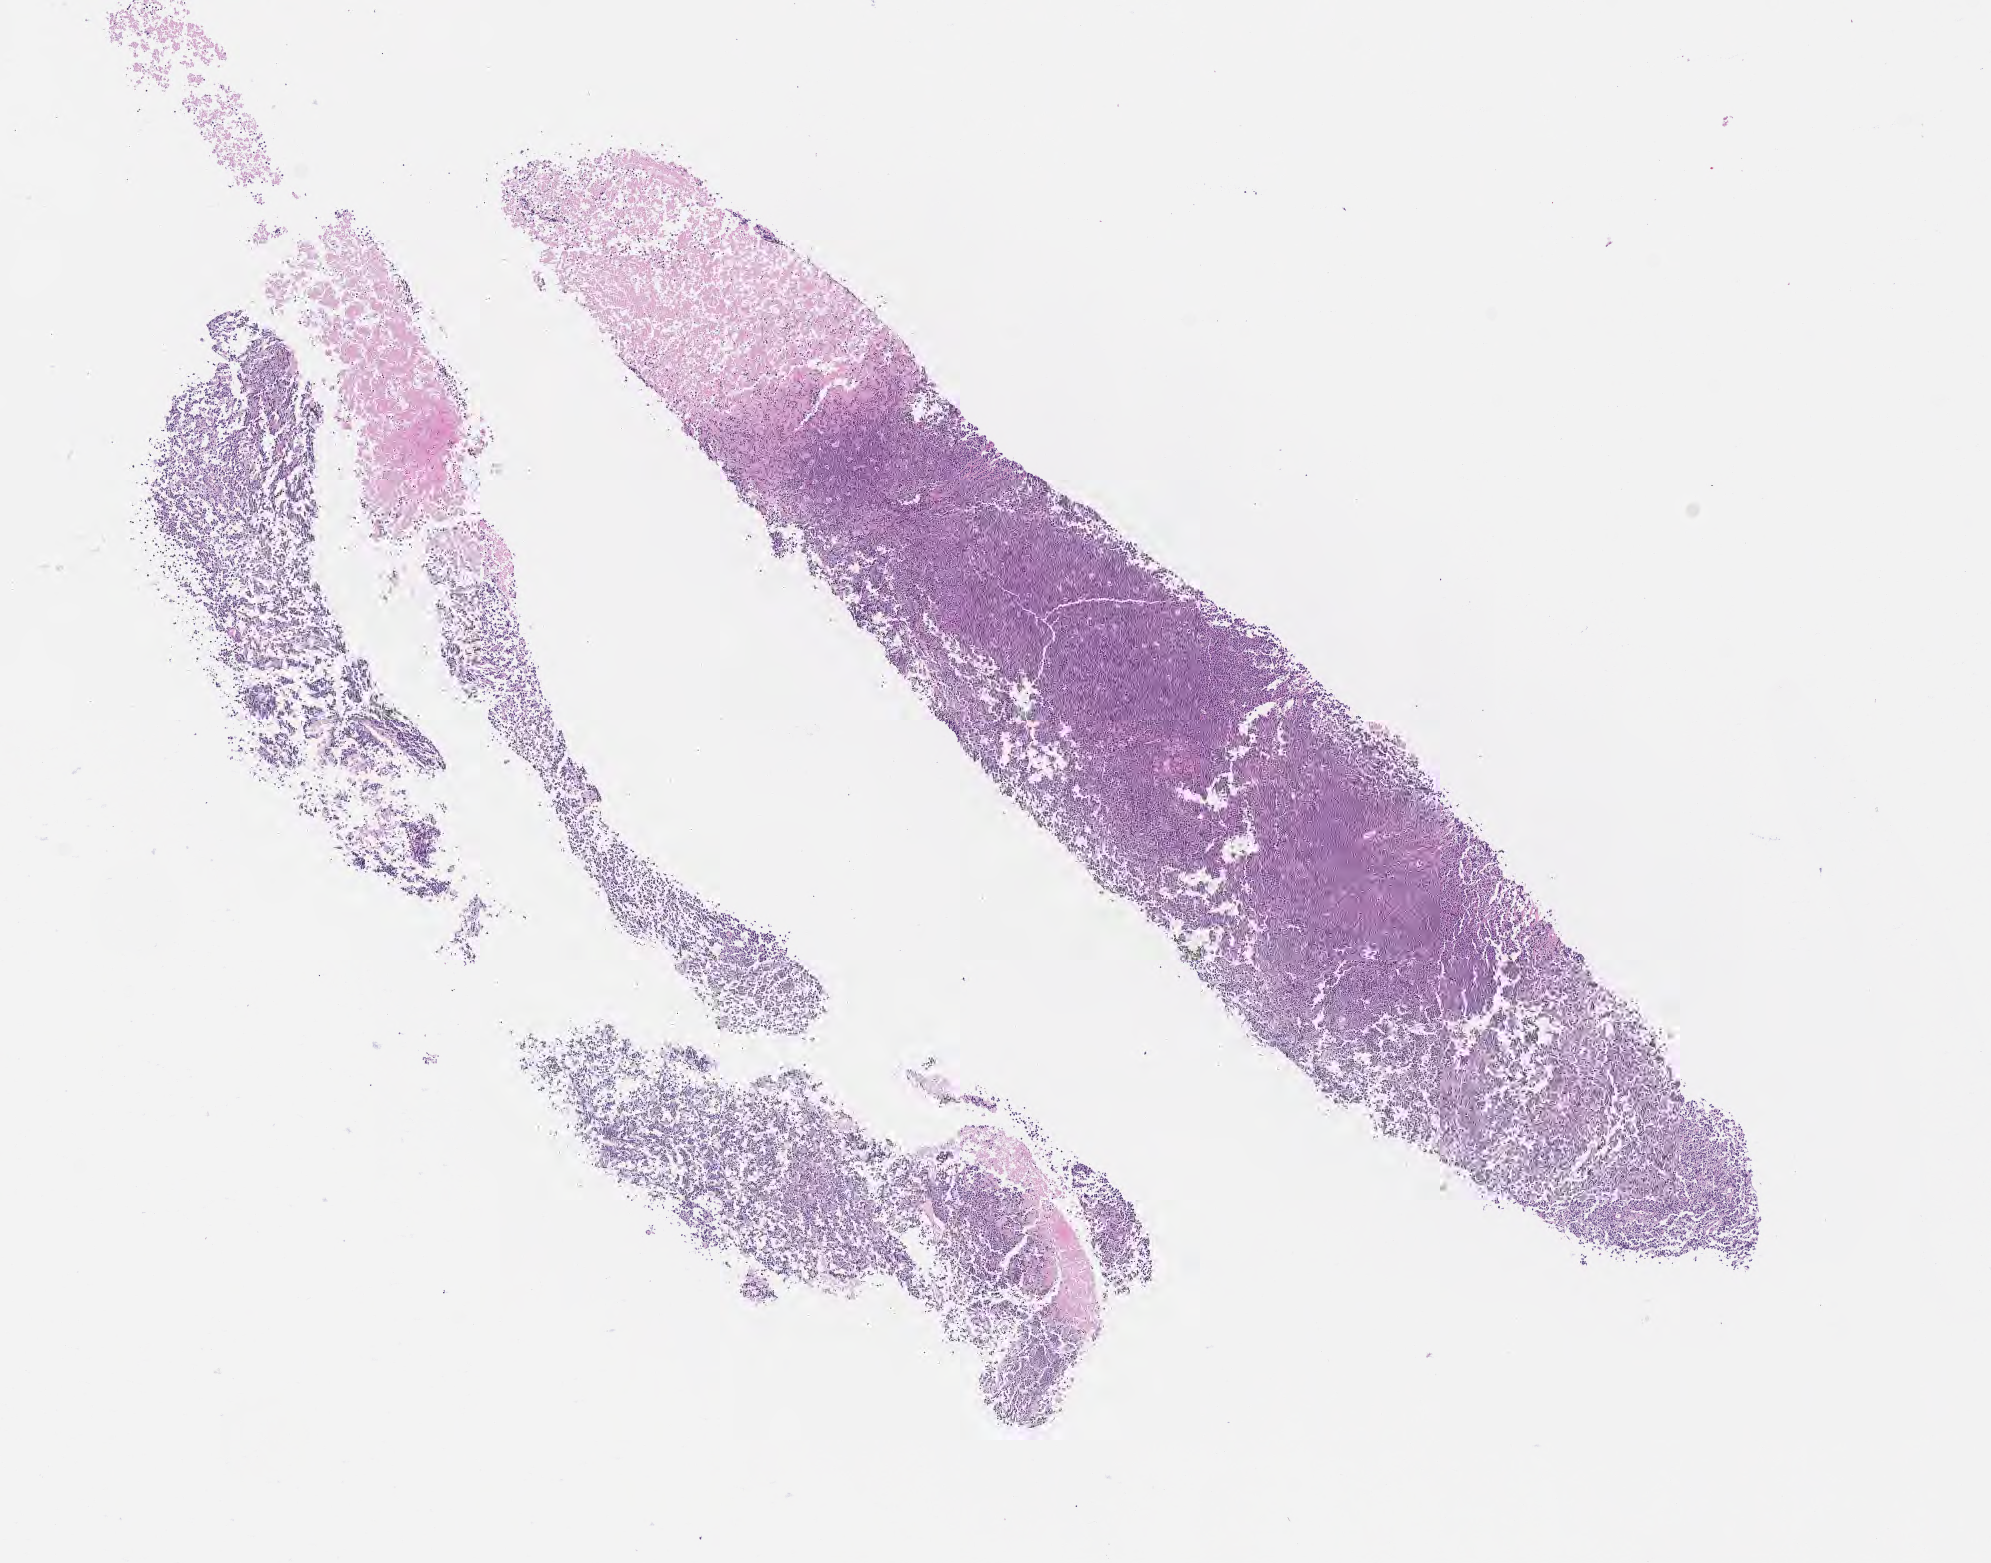
H&E whole-slide image — a low-resolution overview of the entire scanned area, about 8.1 x 6.3 mm, tumor tissue. Female patient, age 18 years.
Diagnosis: Burkitt lymphoma, NOS.